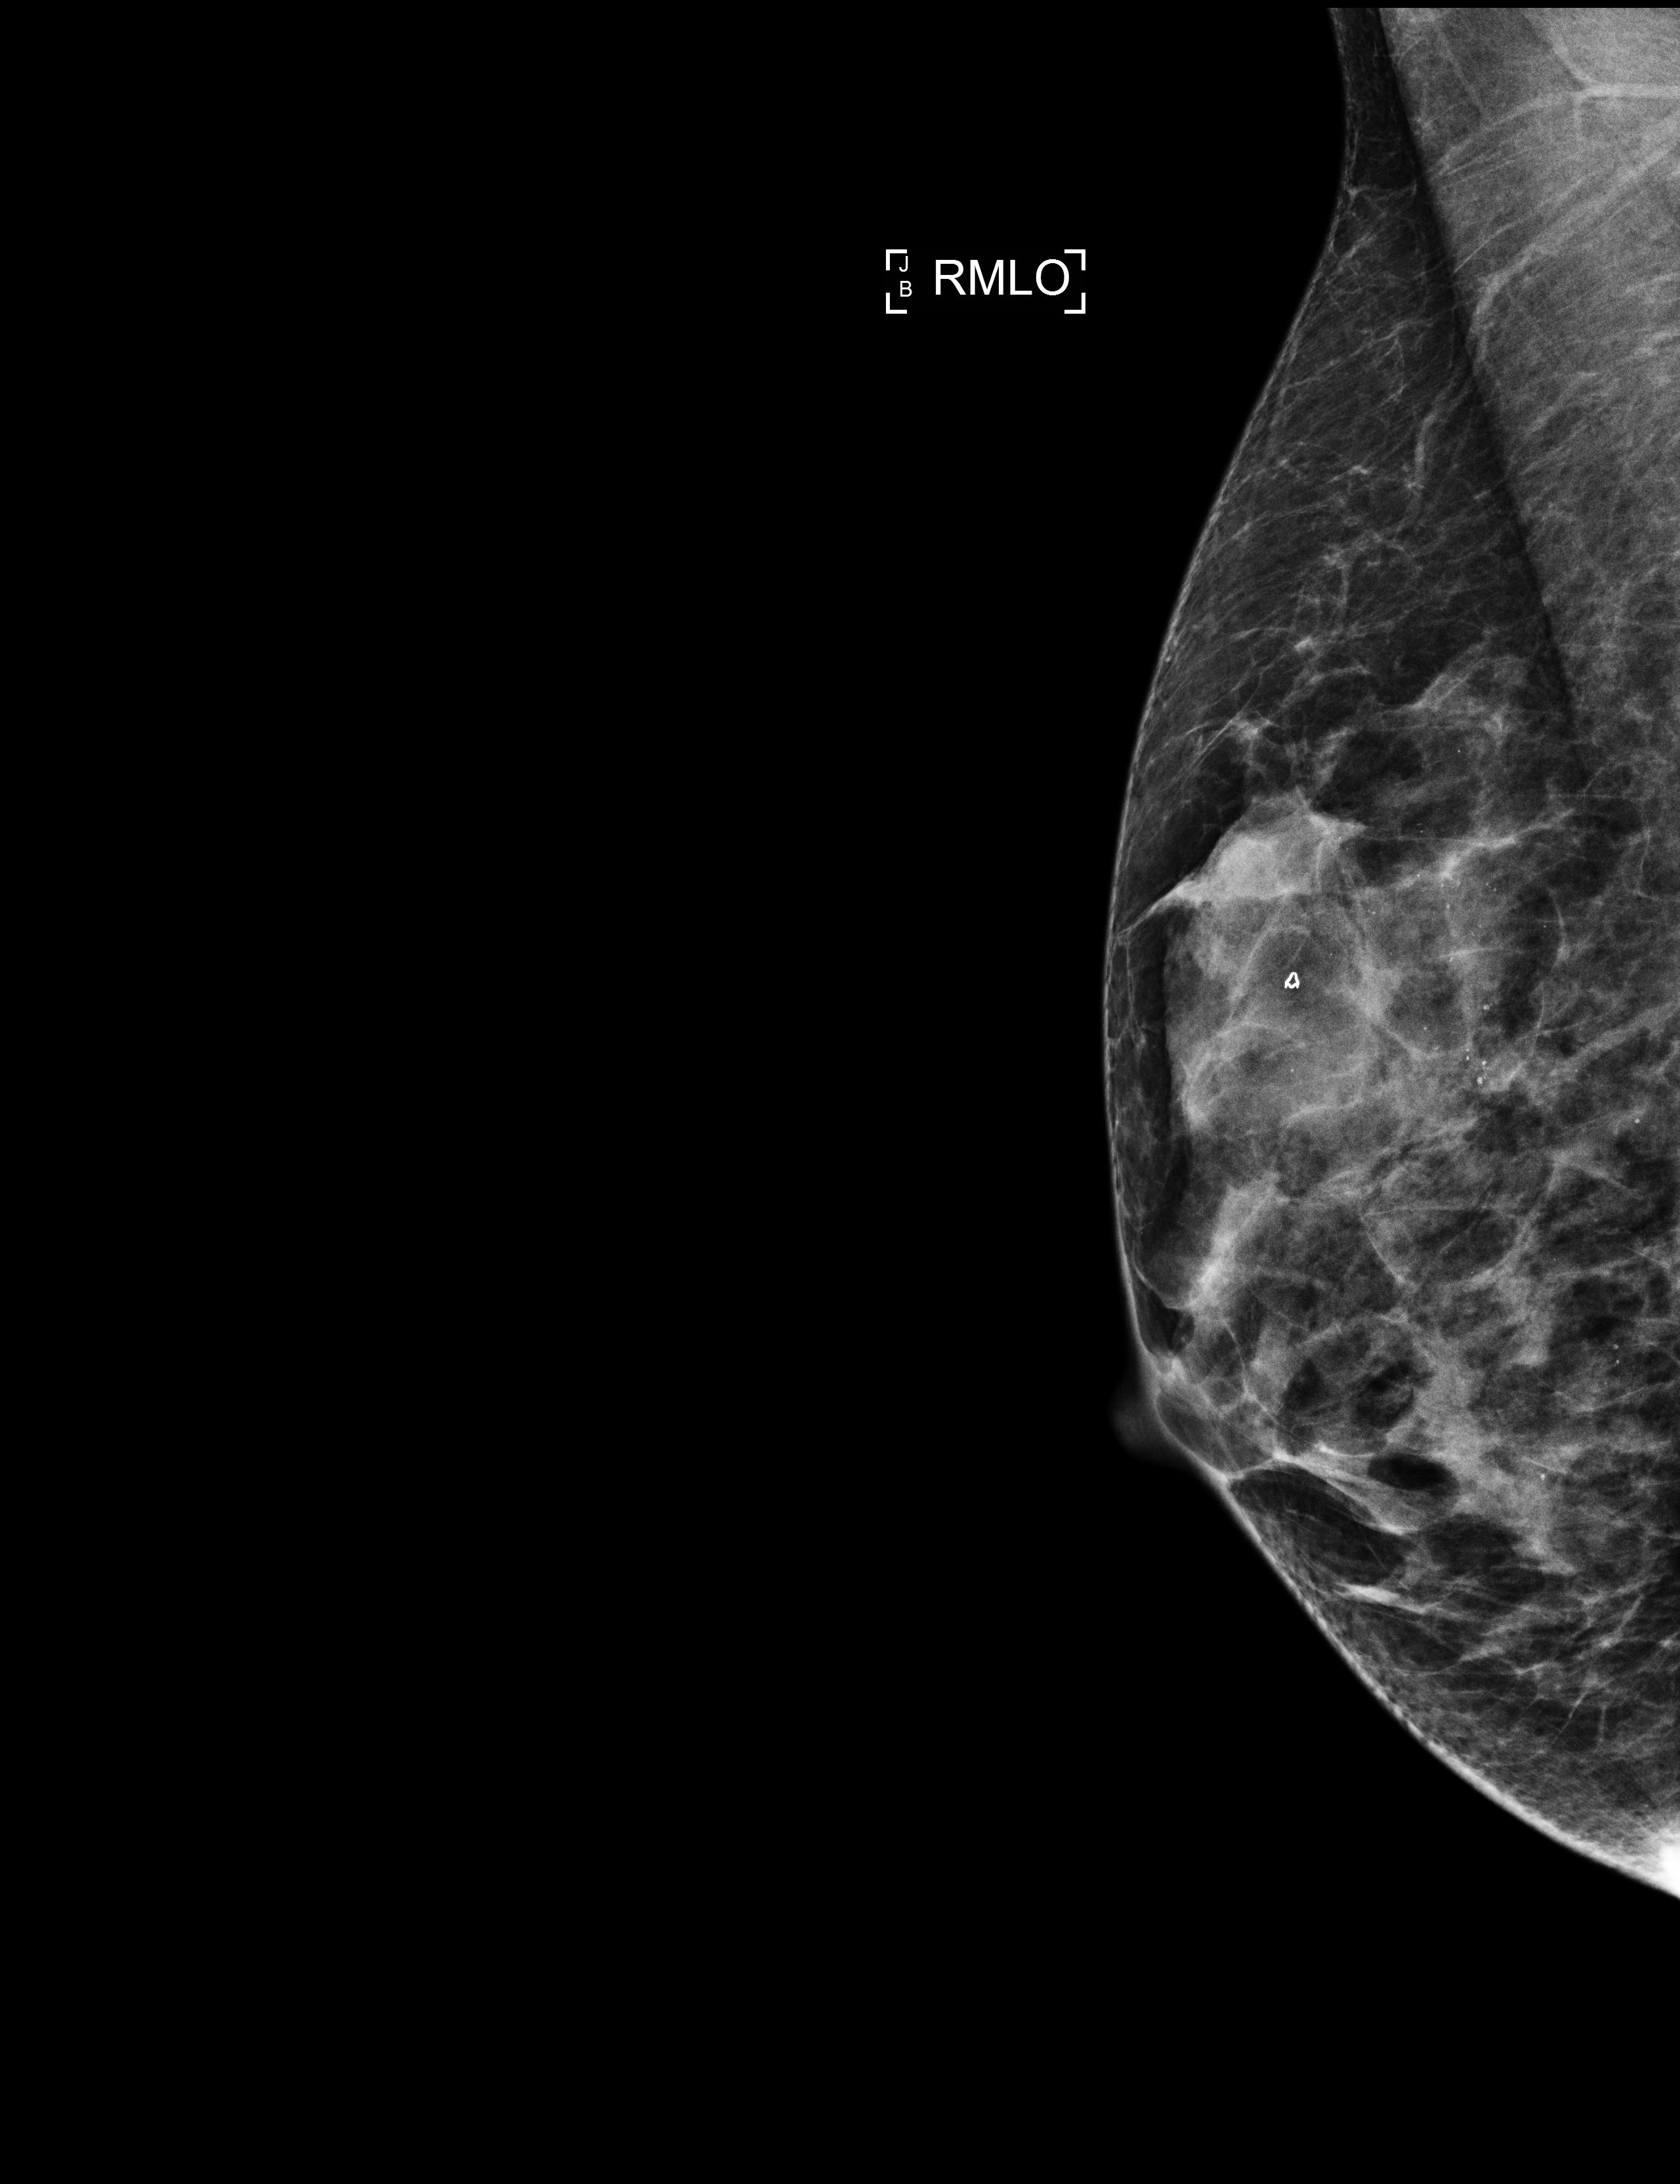
Annual screening mammography examination, system: Selenia Dimensions. Patient aged 58 years (female).
Image type: full-field digital mammogram. Breast: right. Projection: MLO view.